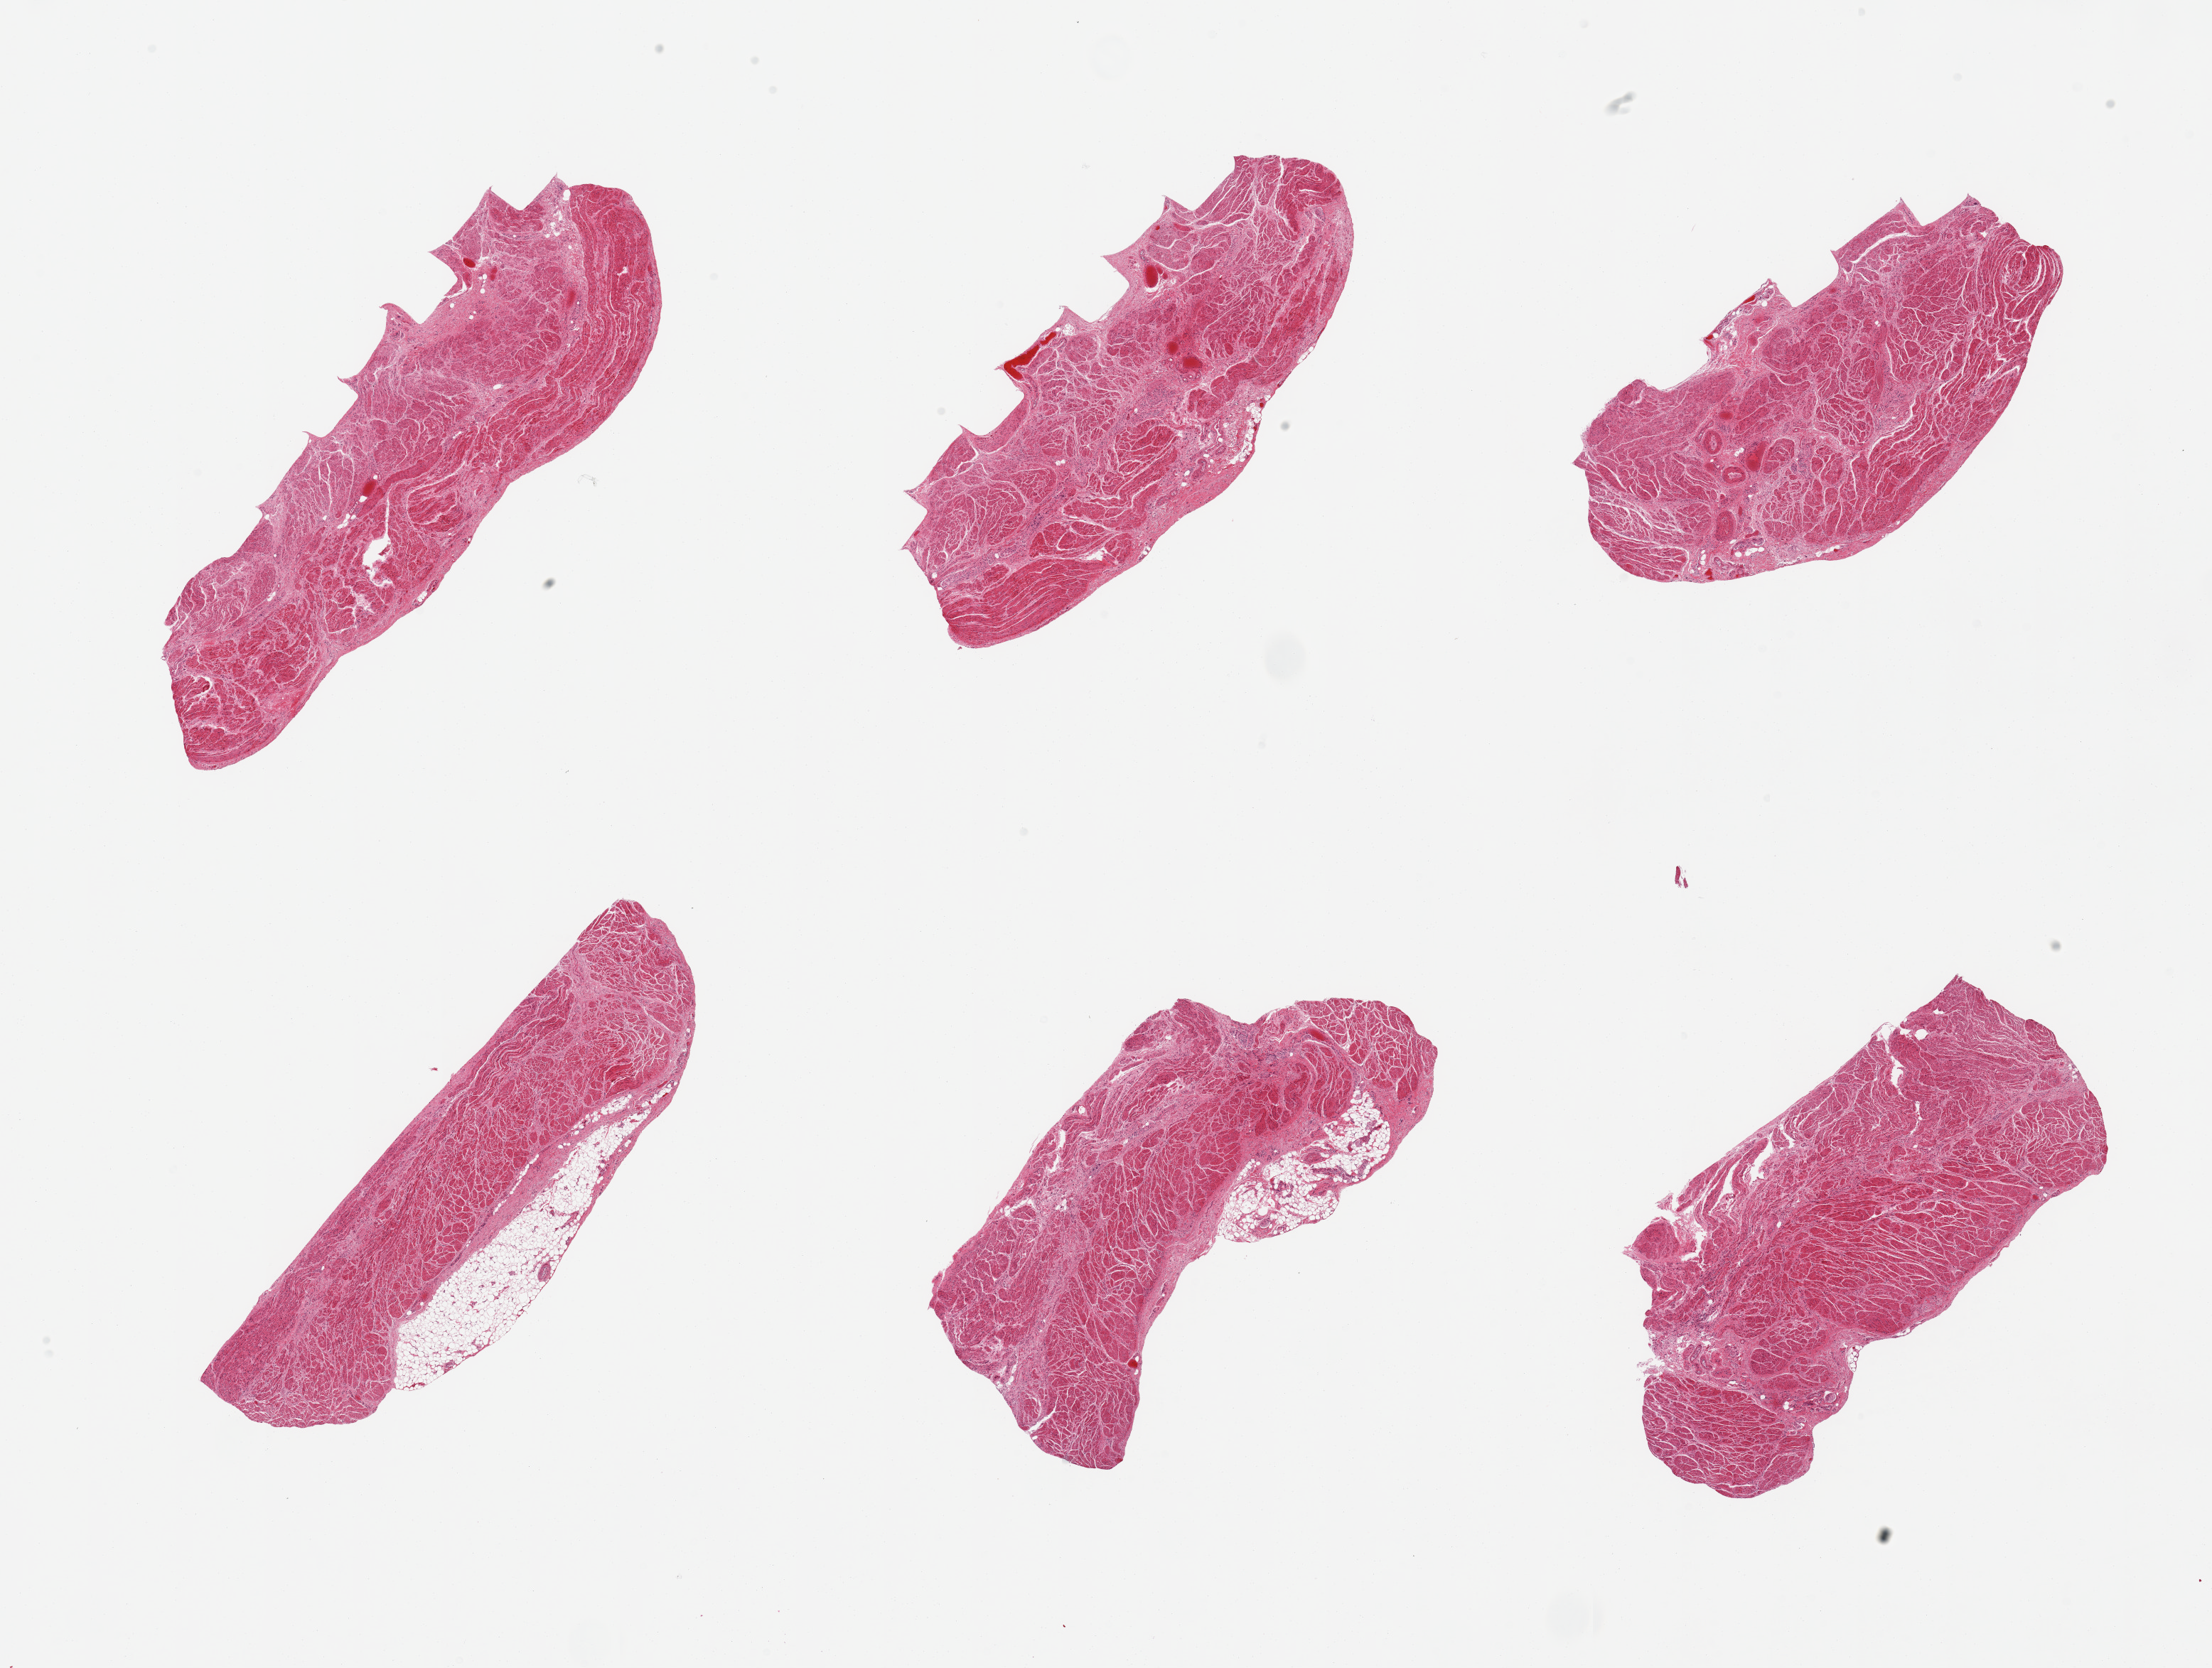
Whole-slide image, hematoxylin and eosin (H&E) stain, shown as a low-resolution overview of the whole scanned area (about 24.6 x 18.6 mm); PAXgene-fixed, paraffin-embedded tissue; target tissue: gastroesophageal junction; tissue donor sample. Male donor.
Reviewer comment on this tissue sample: 6 pieces, target muscularis, few nibbuins of adherent fat.